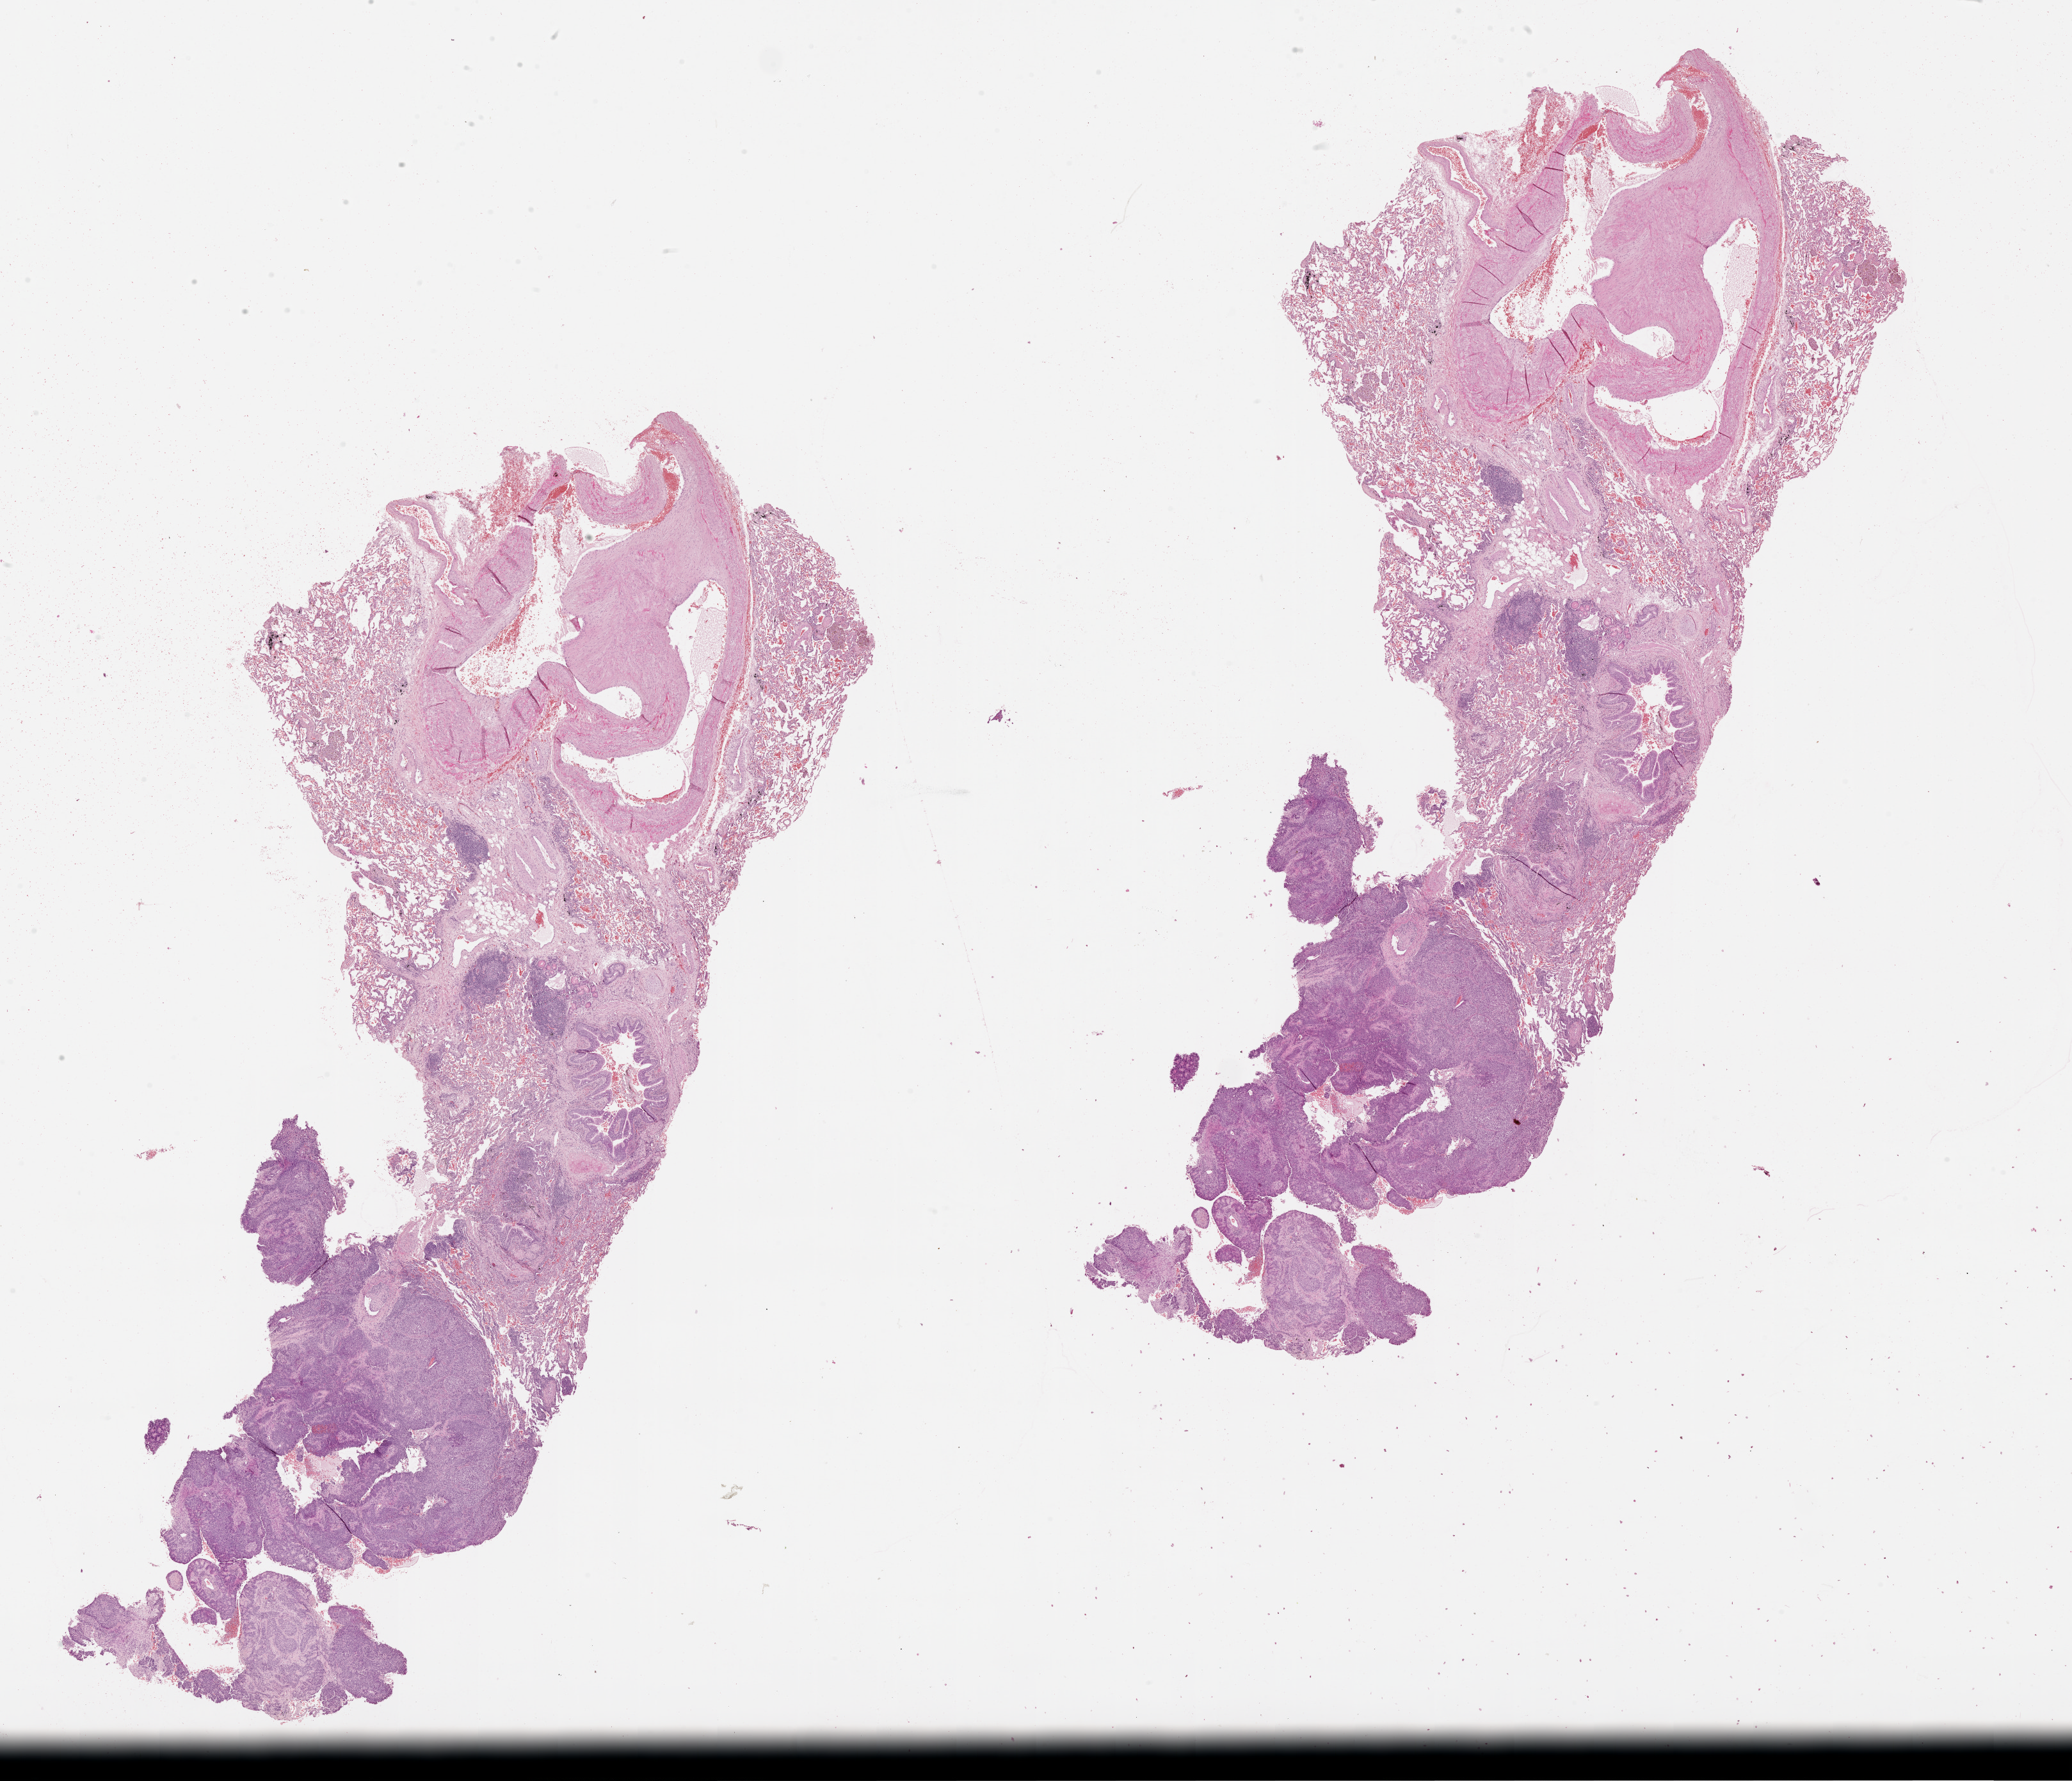
Digitized H&E tissue section (whole slide), shown as a low-resolution overview of the whole scanned area (about 26.1 x 22.4 mm, slide scanned at 20x). Lung, tumour tissue. Patient: male, age 69 years.
• patient diagnosis (cohort enrolment): squamous cell carcinoma (lung)